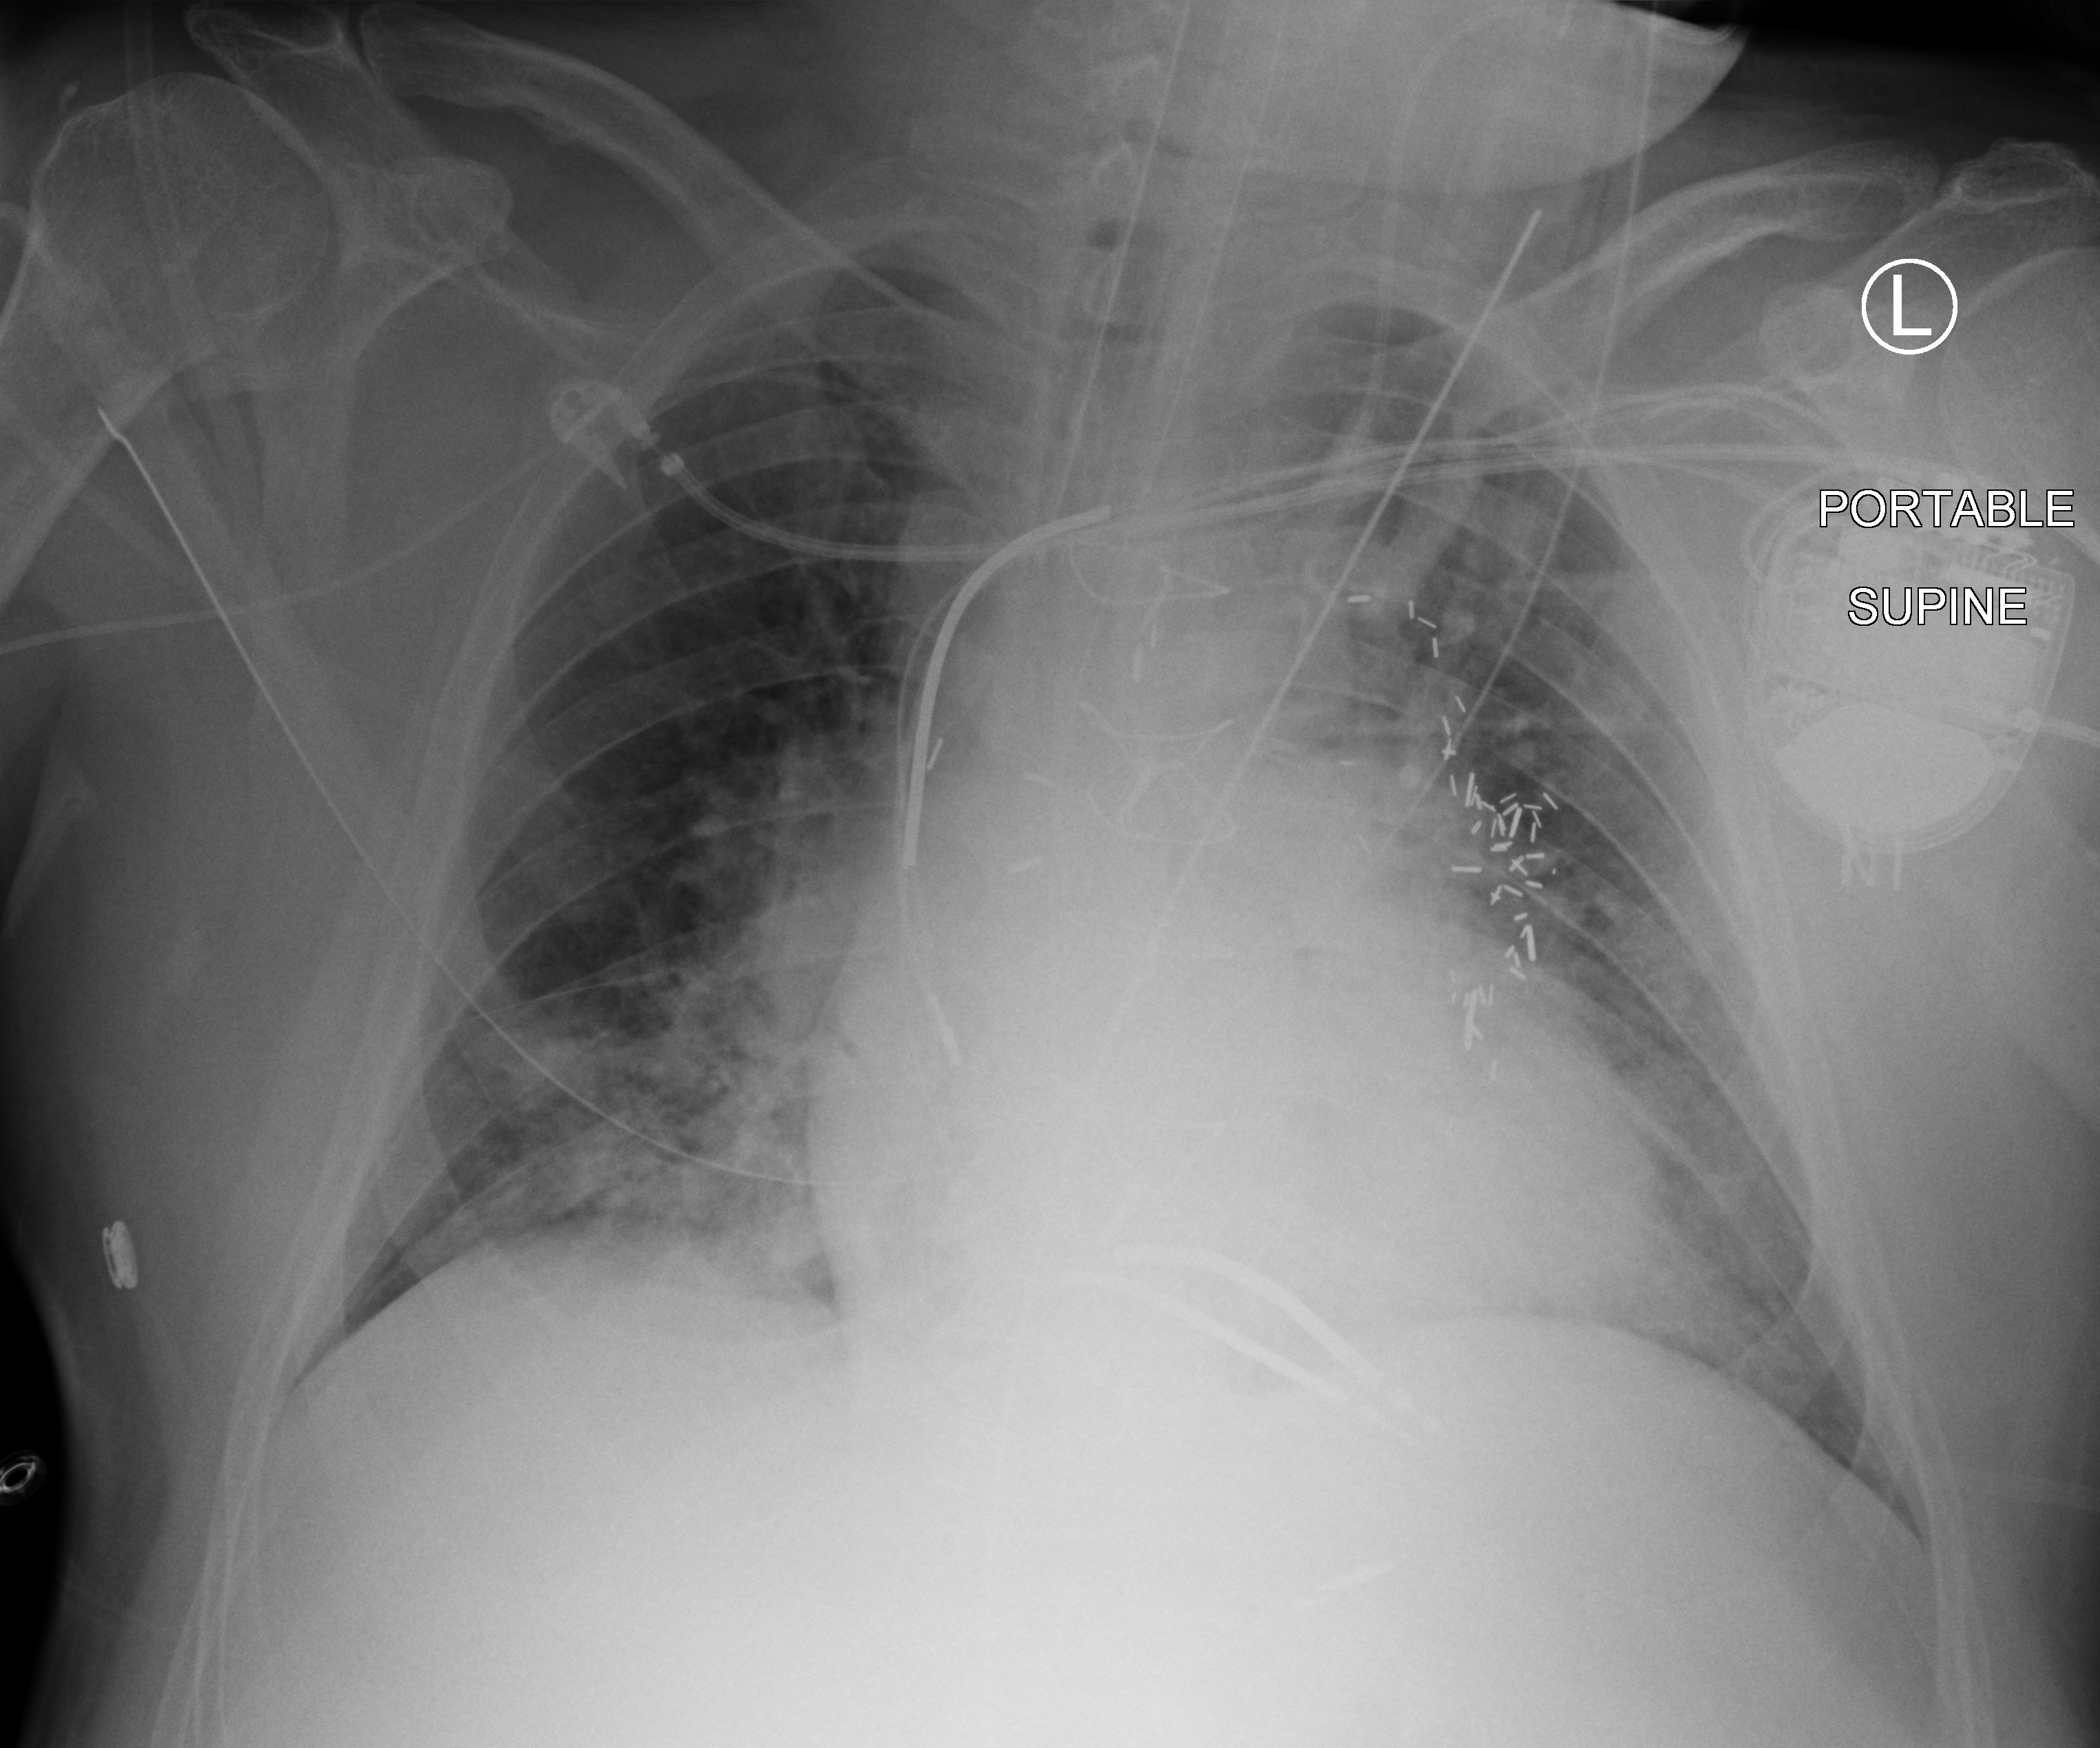
Portable chest radiograph, anteroposterior (AP) projection. Patient hospitalised with COVID-19; male, aged 60–74 years.
From the hospital-stay record, not from the radiograph (when in the stay this image was taken is not recorded):
- admitted to intensive care during this hospital stay: yes
- mechanically ventilated during this hospital stay: yes